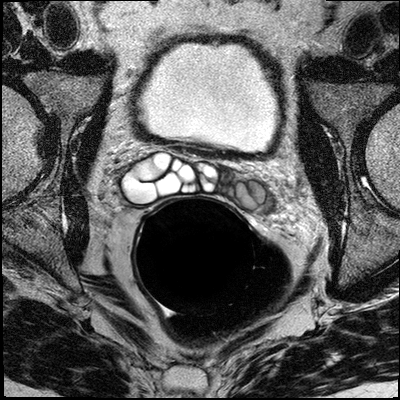
Multiparametric prostate MRI examination; 3 images, each a single mid-volume slice chosen by position (not for content). Treatment context recorded for this patient: No surgery, salvage radiation theraphy.
Image 1: T2-weighted axial slice, series "T2W_TSE_AX", slice 17 of 32.
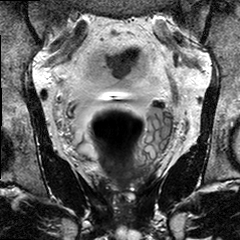
Image 2: T2-weighted coronal slice, slice 13 of 24.
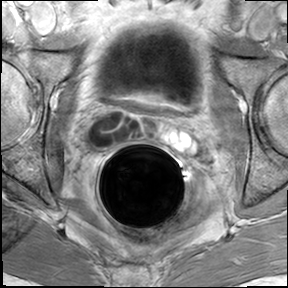
Image 3: axial dynamic contrast-enhanced (DCE) T1-weighted image, slice 17 of 32, dynamic phase 5 of 8.
Report of this MRI examination:
The zonal anatomy is preserved, however there are unusual small
fluid collections along the surgical capsule suggestive or history of
cryo-therapy/HIFU. The maximal craniocaudal diameter 3.5 cm, the
maximal AP diameter of 3.4 cm and maximal transverse diameter of 4.3 cm resulting in an estimated total gland volume of 27 cc. At the base and the mid 3rd of the prostate there is a bulging left posterior
lateral peripheral zone noted, with indistinct capsule towards the
left neuro vascular bundle. Beginning involvement of the left knee
was in the bundle cannot be excluded however due to the apparent post treatment changes this finding is nonspecific. There are no discrete tumor masses seen beyond the capsule. There is no suspicious contrast-enhancement seen beyond the capsule. There is however suspicious enhancement seen within the left peripheral zone of the base mid 3rd and apical third between 3 and 6 o'clock, at the mid 3rd level suspicious enhancement crosses the midline and involves the paramedian left and right peripheral zone. The right neural was combined with is free. The left seminal vesicles show T2 relative hypo intense and T1 right prior intense signal suggestive or protein Rich content/ hemorrhage/ amyloidosis. No intraluminal or intramural nodularity or suspicious enhancement is seen within the seminal vesicles of the left and right side. No pelvic lymphadenopathy. IMPRESSION: Predominantly left-sided prostate cancer the posterior-lateral peripheral zone adjacent to the left neurovascular bundle, without evidence of manifest extracapsular extension on either side; however beginning capsular infiltration cannot be excluded on the background of apparent post treatment changes, suggestive for a history of cryotherapy. No evidence of involvement of the right neurovascular bundle. Left hemorrhagic/protein rich seminal vesicles; no evidence of seminal vesicle infiltration on either side. No pelvic lymphadenopathy

Prostate biopsy pathology (as recorded):
PROSTATE: 1. RIGHT PZ:PROSTATIC ADENOCARCINOMA, GLEASON SCORE 3+3=6/10, INVOLVING <5% OF TISSUE SUBMITTED. 2. RIGHT PZ/TZ:PROSTATIC TISSUE WITH CHRONIC INFLAMMATION.NO TUMOR IDENTIFIED. 3. RIGHT APEX: PROSTATIC TISSUE WITH CHRONIC INFLAMMATION. NO TUMOR IDENTIFIED 4. LEFT PZ: PROSTATIC TISSUE, NO TUMOR IDENTIFIED. 5. LEFT PZ/TZ: PROSTATIC ADENOCARCINOMA, GLEASON SCORE 3+3=6/10, INVOLVING 20% OF TISSUE SUBMITTED. 6. LEFT APEX: PROSTATIC TISSUE, NO TUMOR IDENTIFIED. 7. FLOATER: PROSTATIC TISSUE WITH CHRONIC INFLAMMATION. NO TUMOR IDENTIFIED.